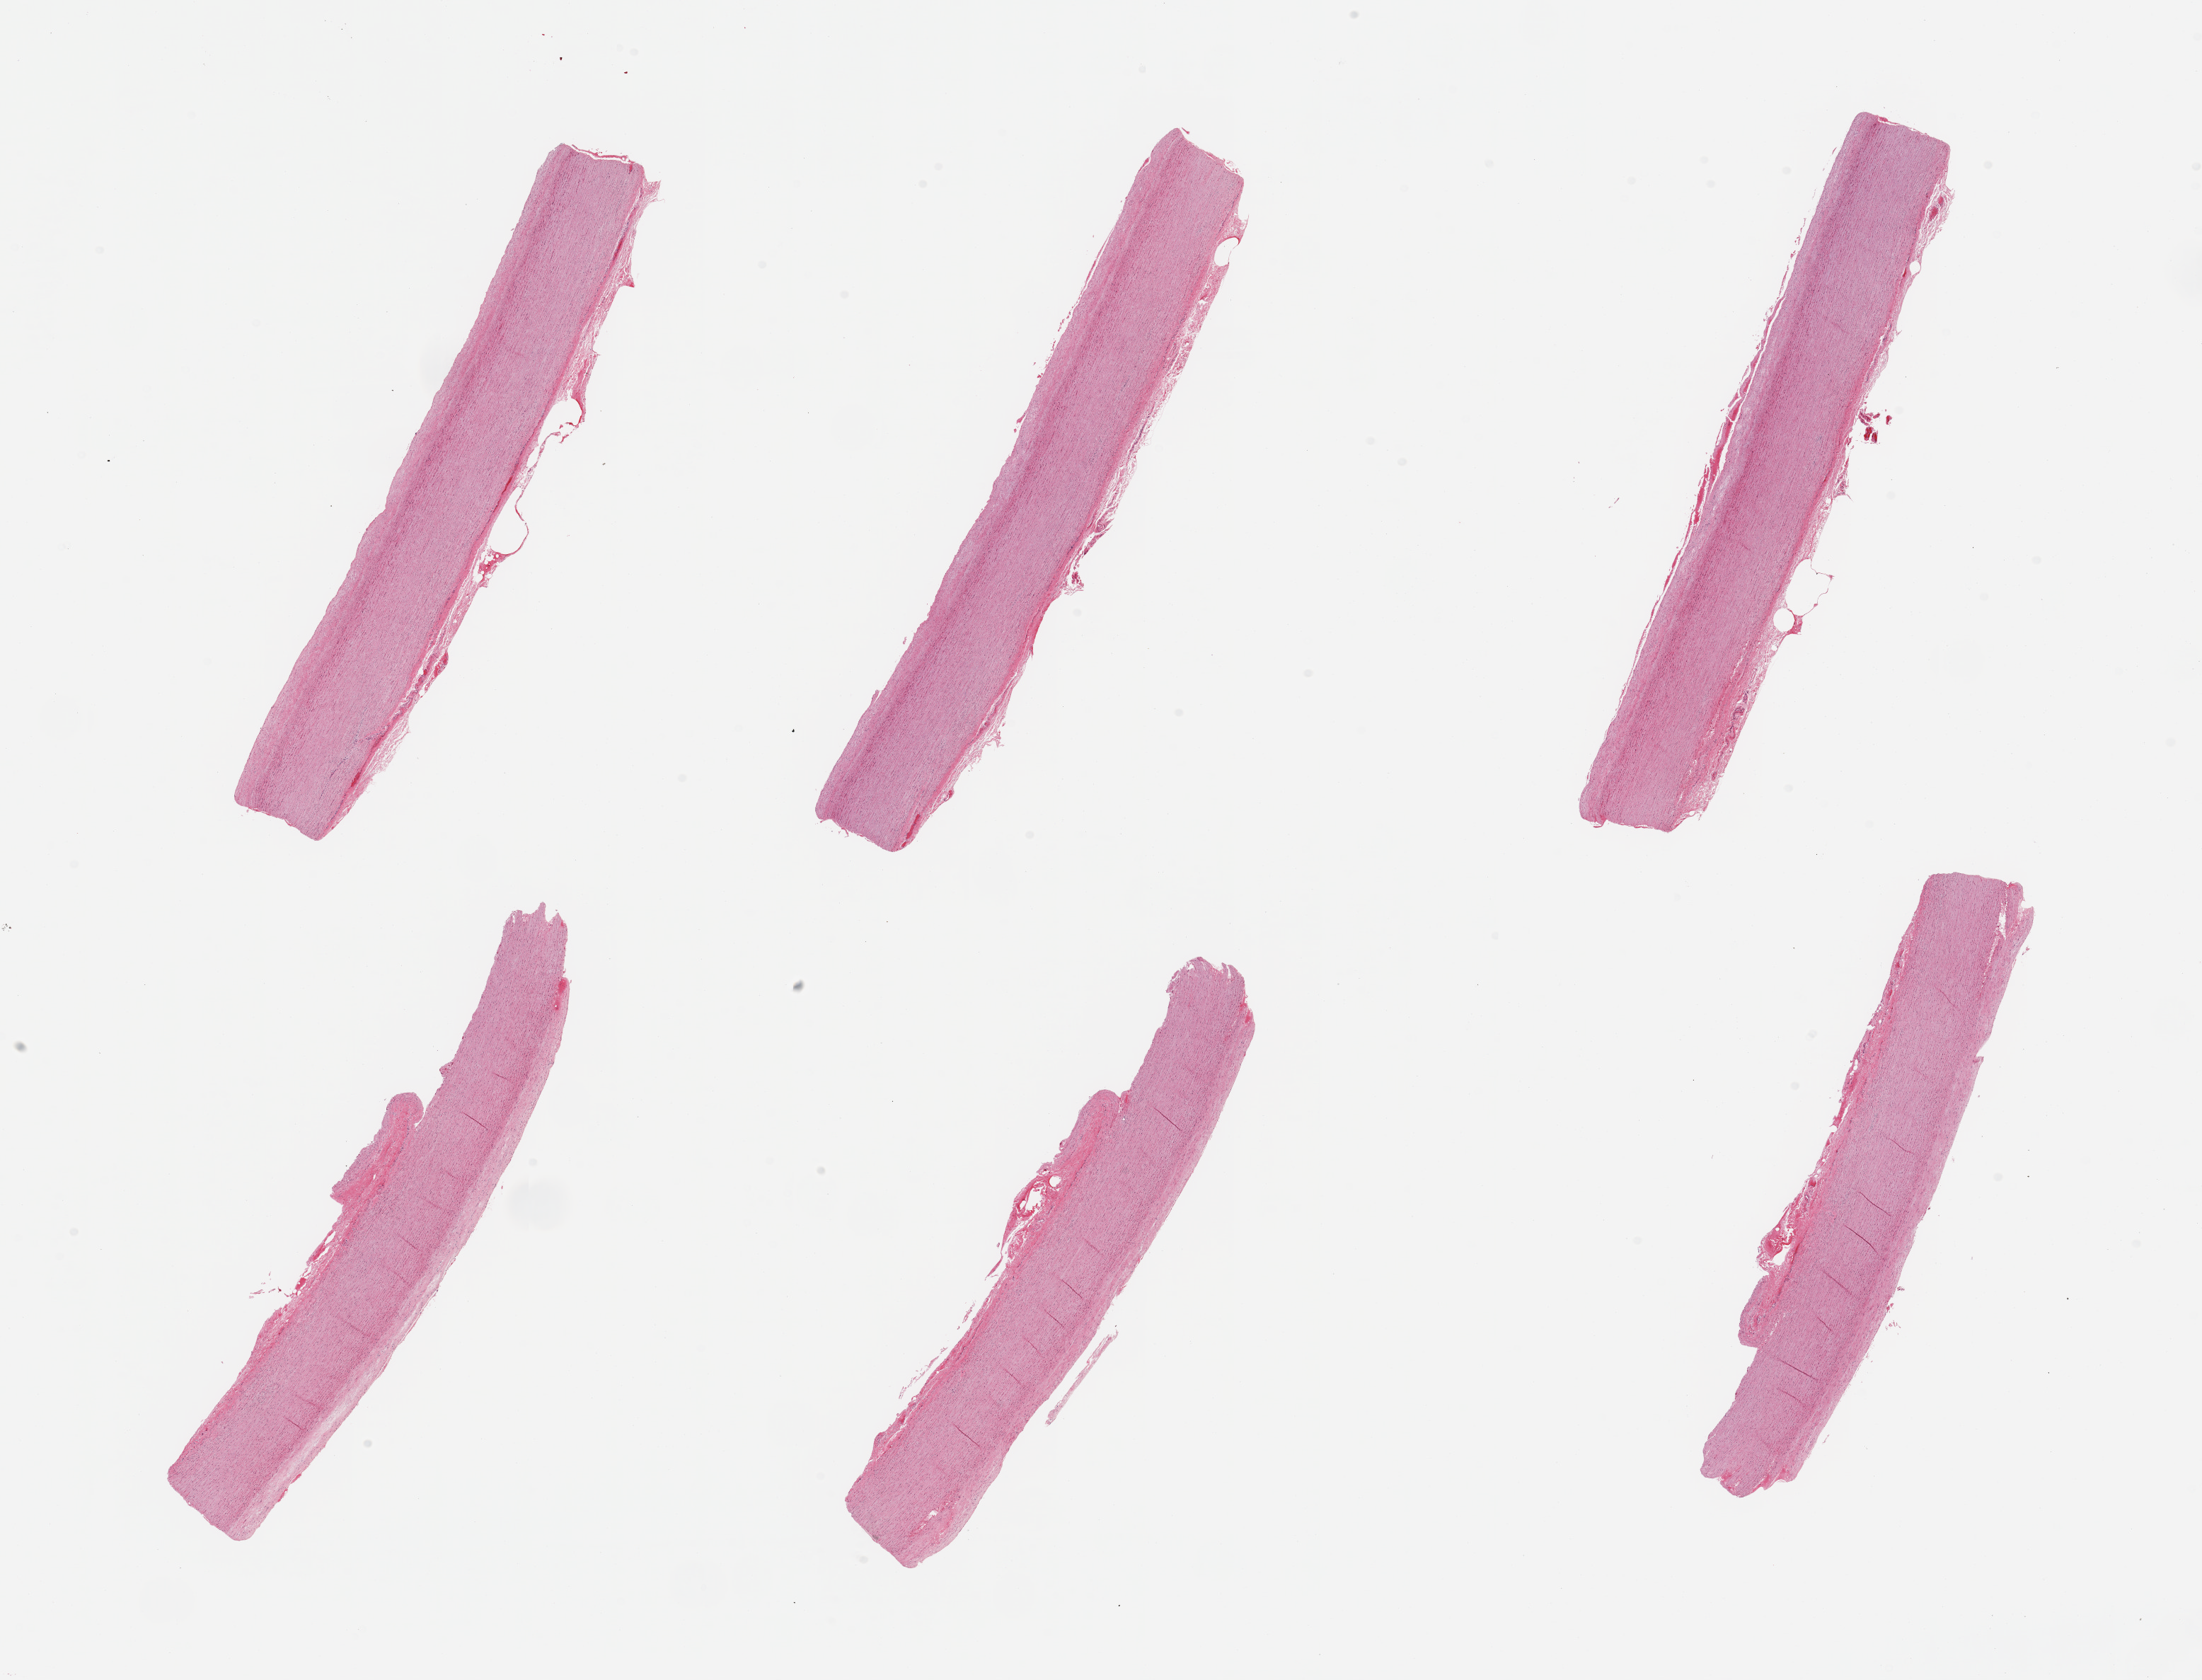
Whole-slide image, hematoxylin and eosin (H&E) stain — shown as a low-resolution overview of the whole scanned area (about 24.6 x 18.8 mm, acquisition: 20x scan); PAXgene-fixed paraffin-embedded (PFPE) section; sampled site (target tissue): aorta; donor tissue sample. Donor sex: female.
Pathologist's review note for this sample: 6 pieces, lamintated atherosis up to ~0.25mm.